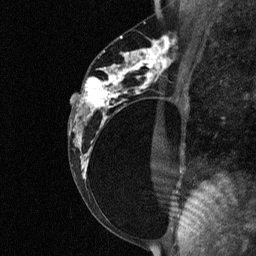
Breast MRI (dynamic contrast-enhanced), one sagittal slice. Position 35 of 64 along the scan axis. Dynamic contrast-enhanced study with each time point stored as its own series, time point 2 of 3 at this slice position (early post-contrast, ordered by acquisition time). 1.5 T. TE 4.8 ms, TR 27 ms. 256 × 256 image matrix. Female patient, age 34 years. Case-level facts recorded for this patient, not image findings: setting: breast cancer imaged before/during neoadjuvant chemotherapy; receptor status: HR-positive, HER2-negative.
Outlined on this slice (semi-automatic segmentation, software-assisted and operator-edited):
- analysis volume of interest (the breast-tissue region the enhancement analysis was run in; not a lesion): bounding box [x1, y1, x2, y2] px = [78, 44, 181, 191]
- tumour enhancement mask (voxels above the 90 % enhancement threshold inside the analysis volume of interest): [82, 44, 169, 167]